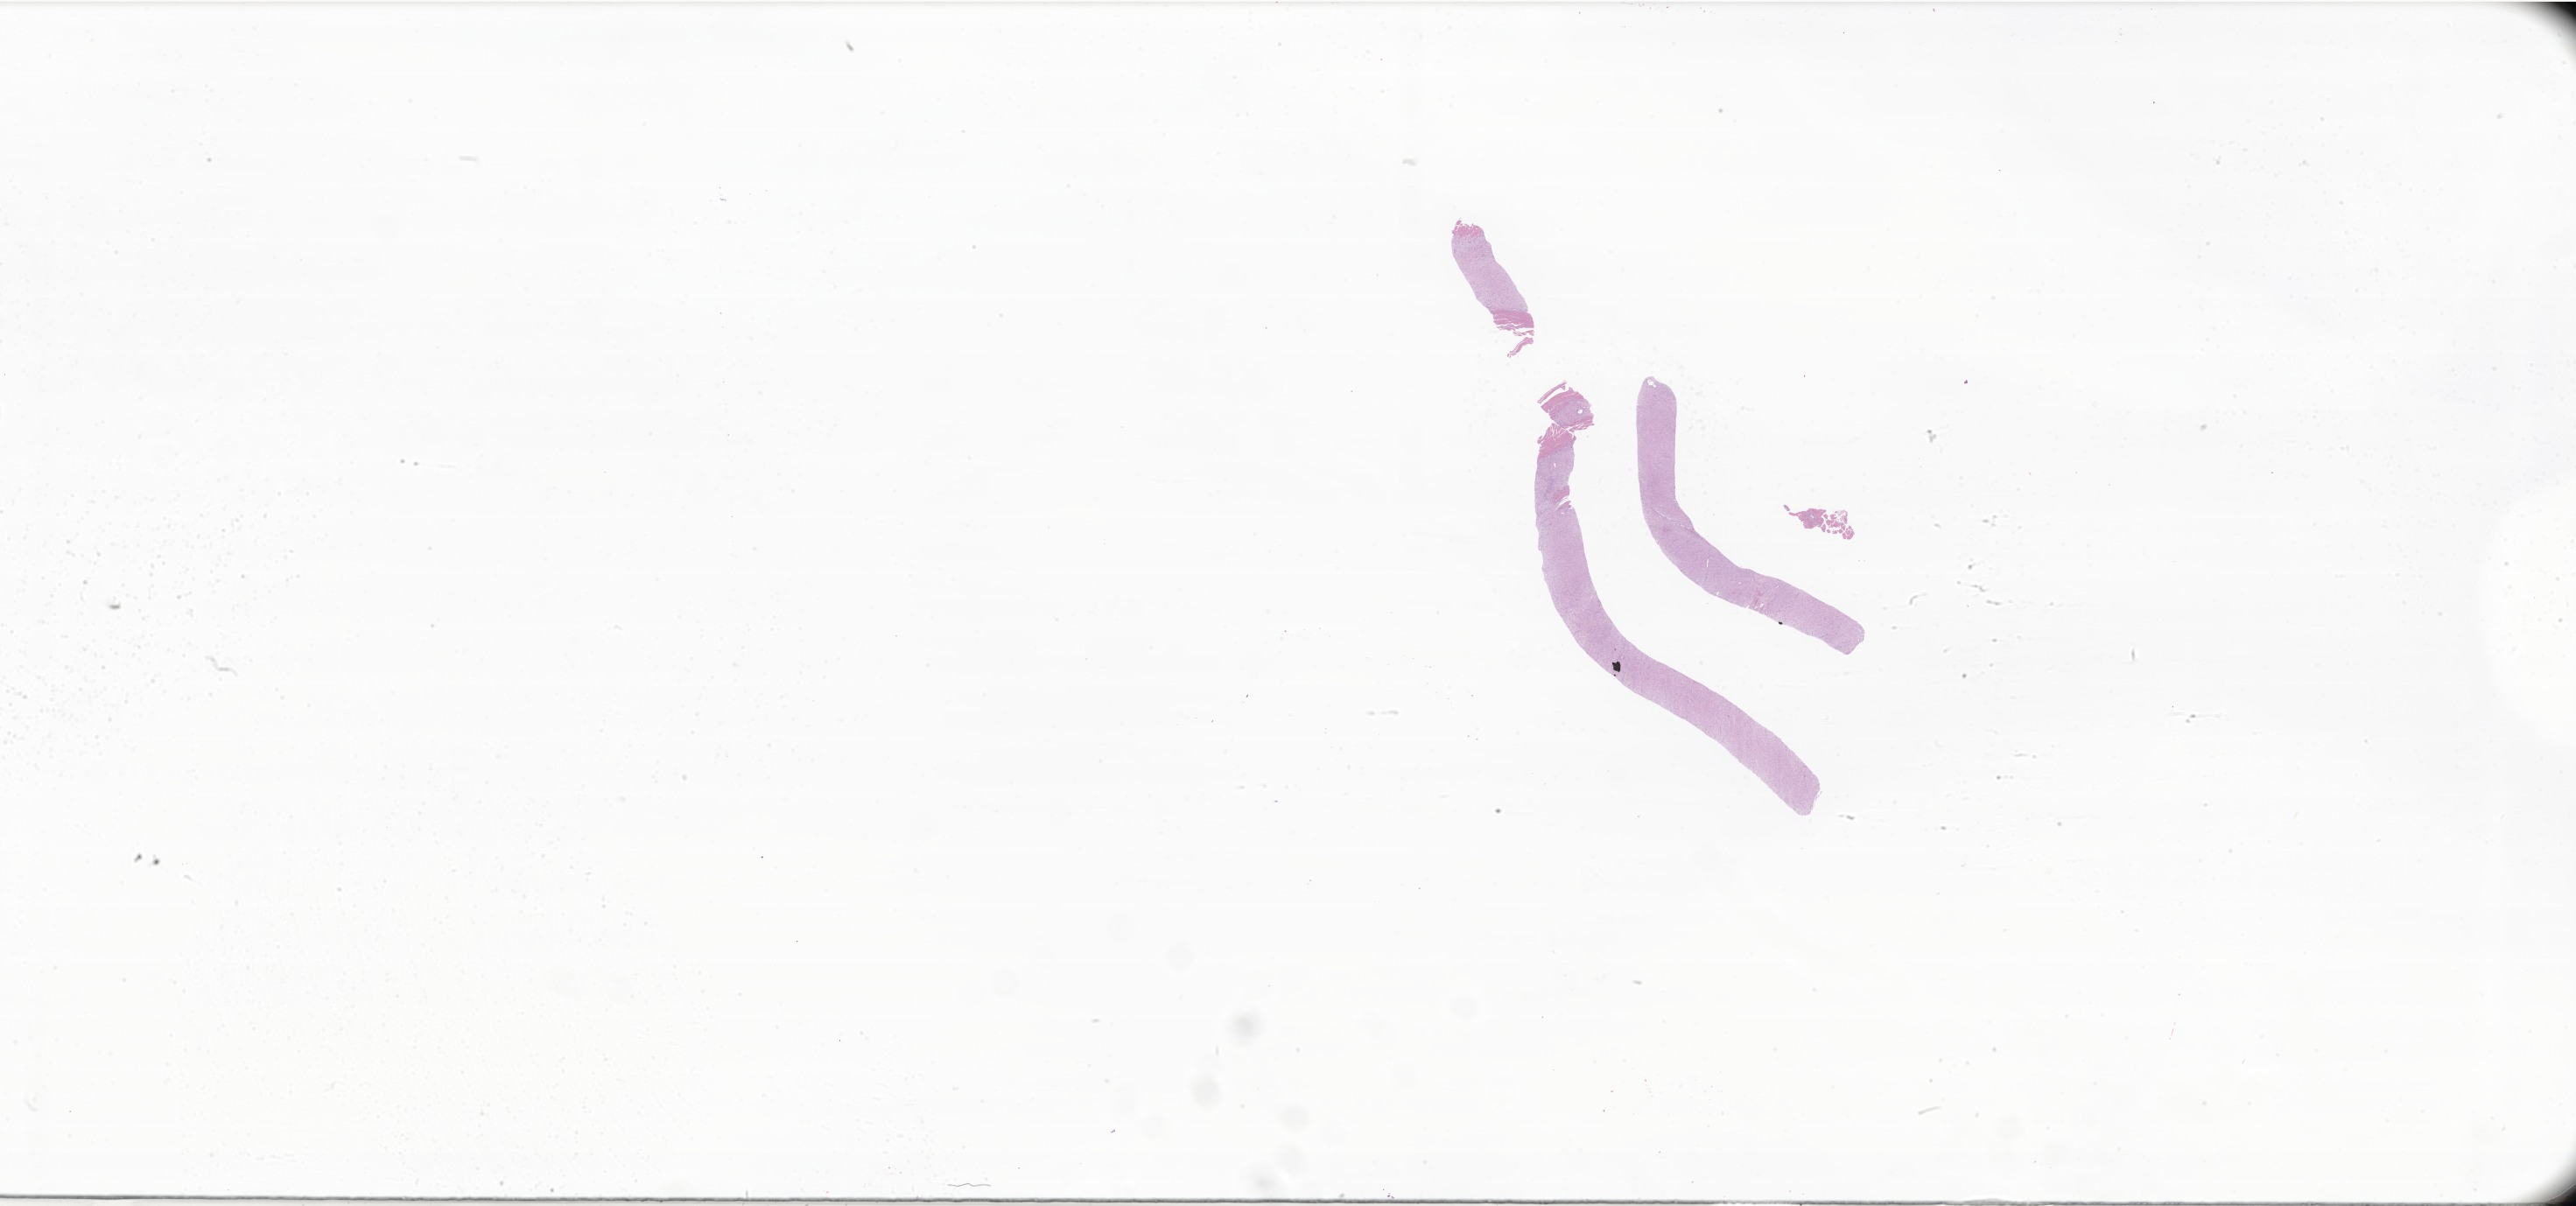
Digitized H&E-stained section of tumor tissue from the soft tissue of lower extremity, low-resolution overview of the scanned area, about 49.6 x 23.2 mm. Male patient, age 209 months (17 years 5 months).
Specimen: FFPE section.